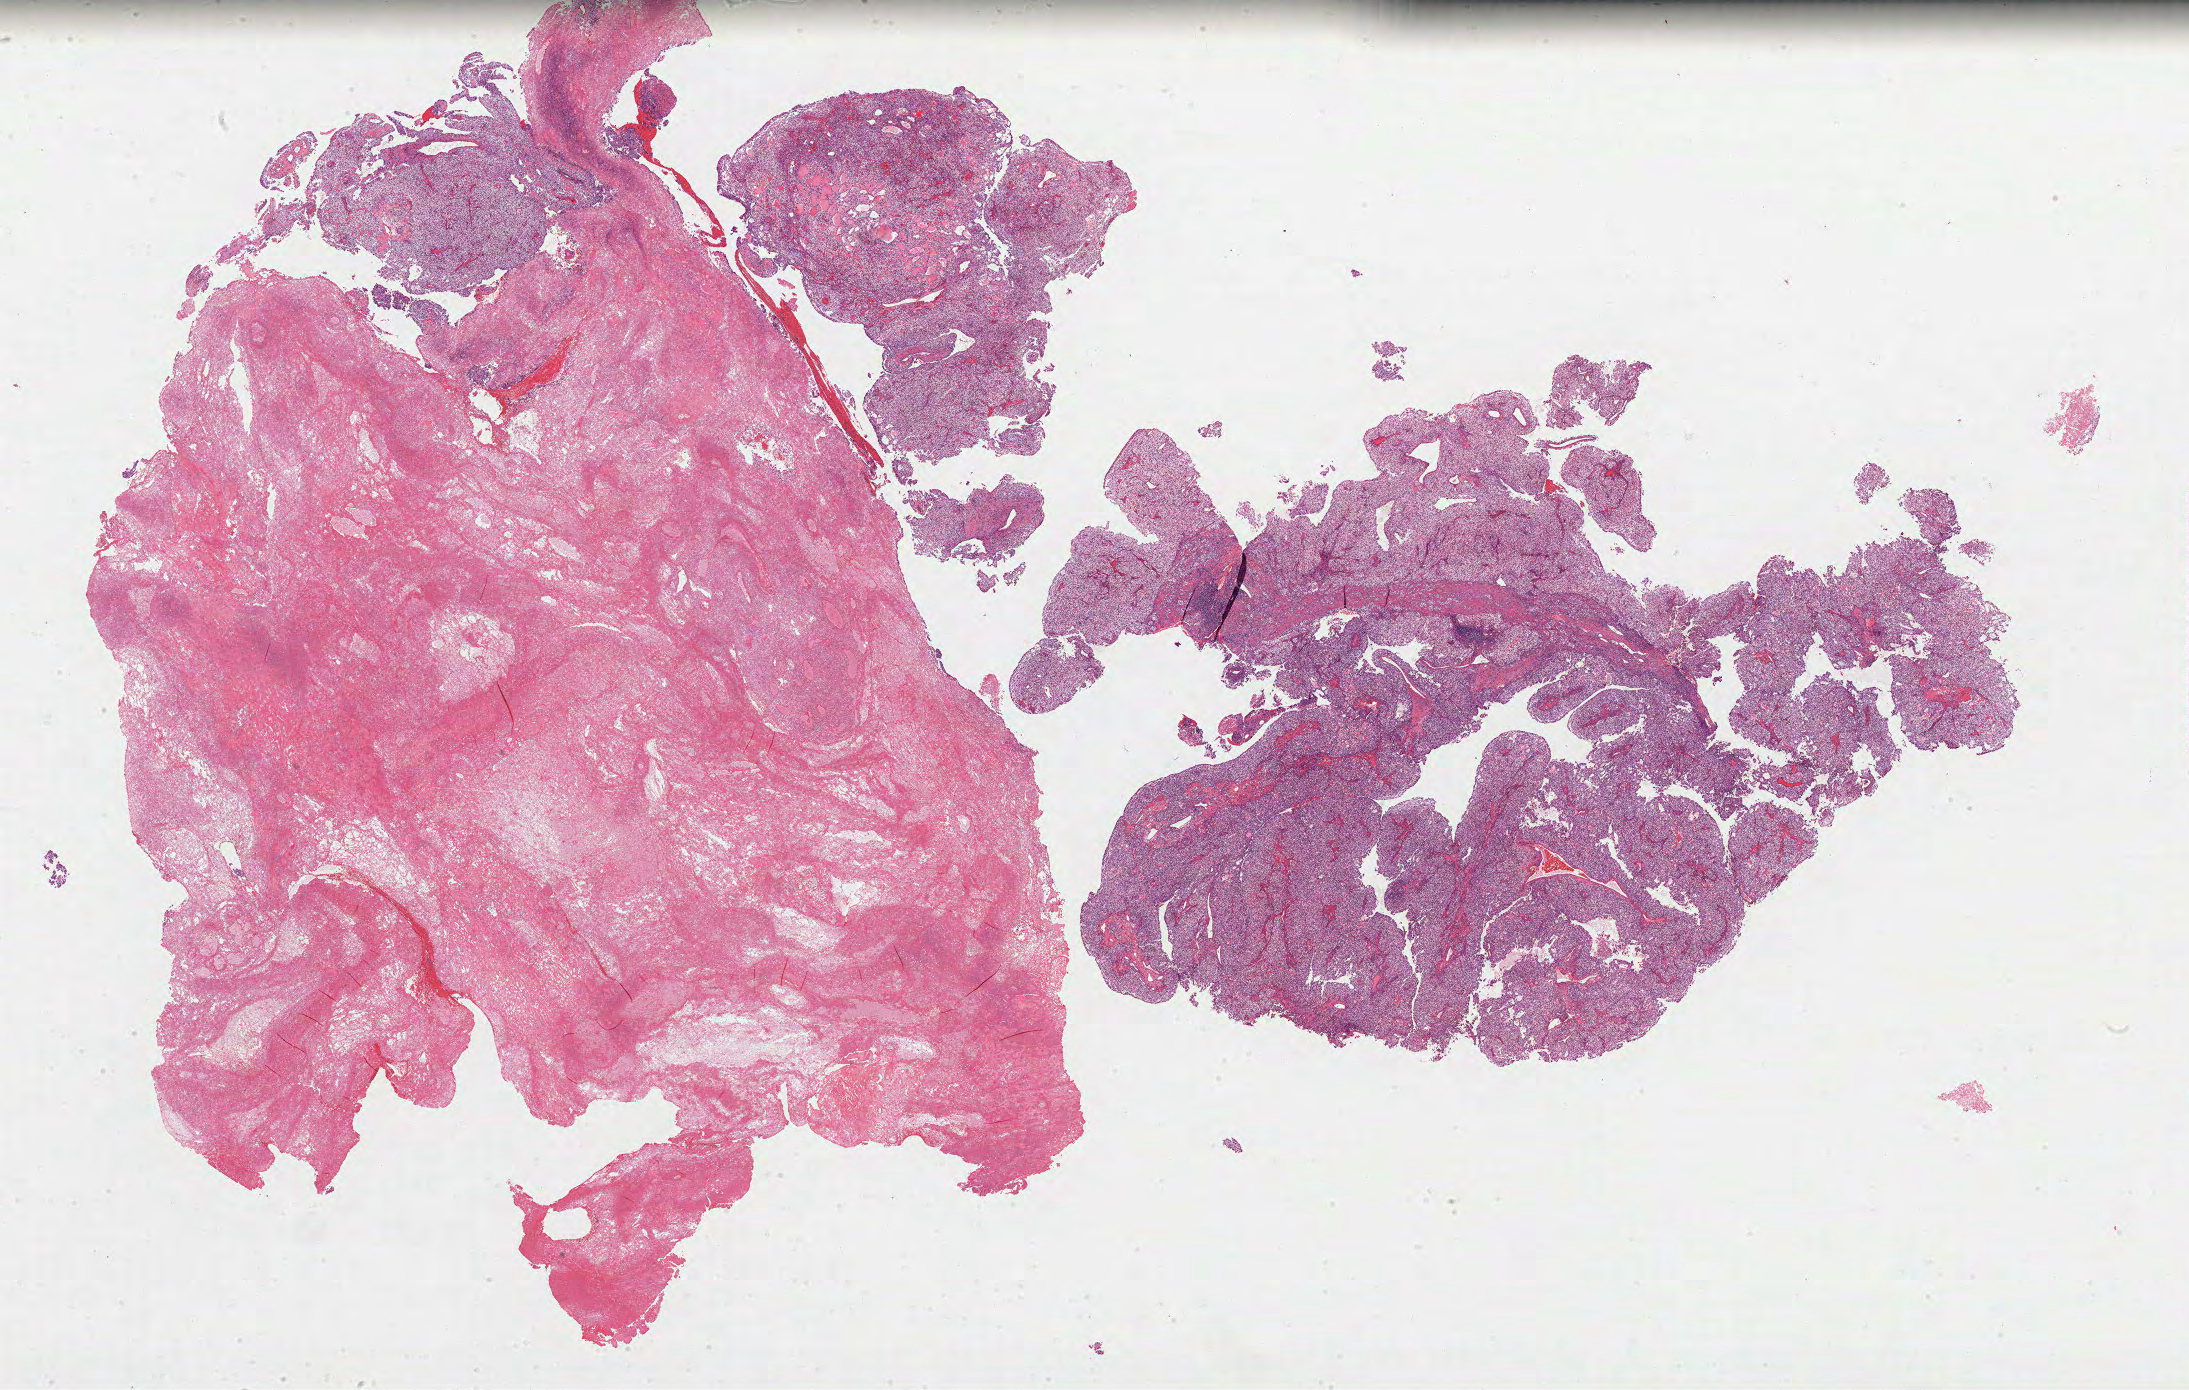
Whole-slide histology image, H&E-stained — low-resolution overview of the scanned area, about 35.3 x 22.4 mm; formalin-fixed paraffin-embedded (FFPE) diagnostic section; sample: primary tumour, kidney. Male, age 41 years at initial diagnosis. Histologic grade: G2 (moderately differentiated).
AJCC pathologic stage: II. Histologic diagnosis: Clear cell adenocarcinoma, NOS. Lymph nodes positive (case pathology): 0 of 16 examined.